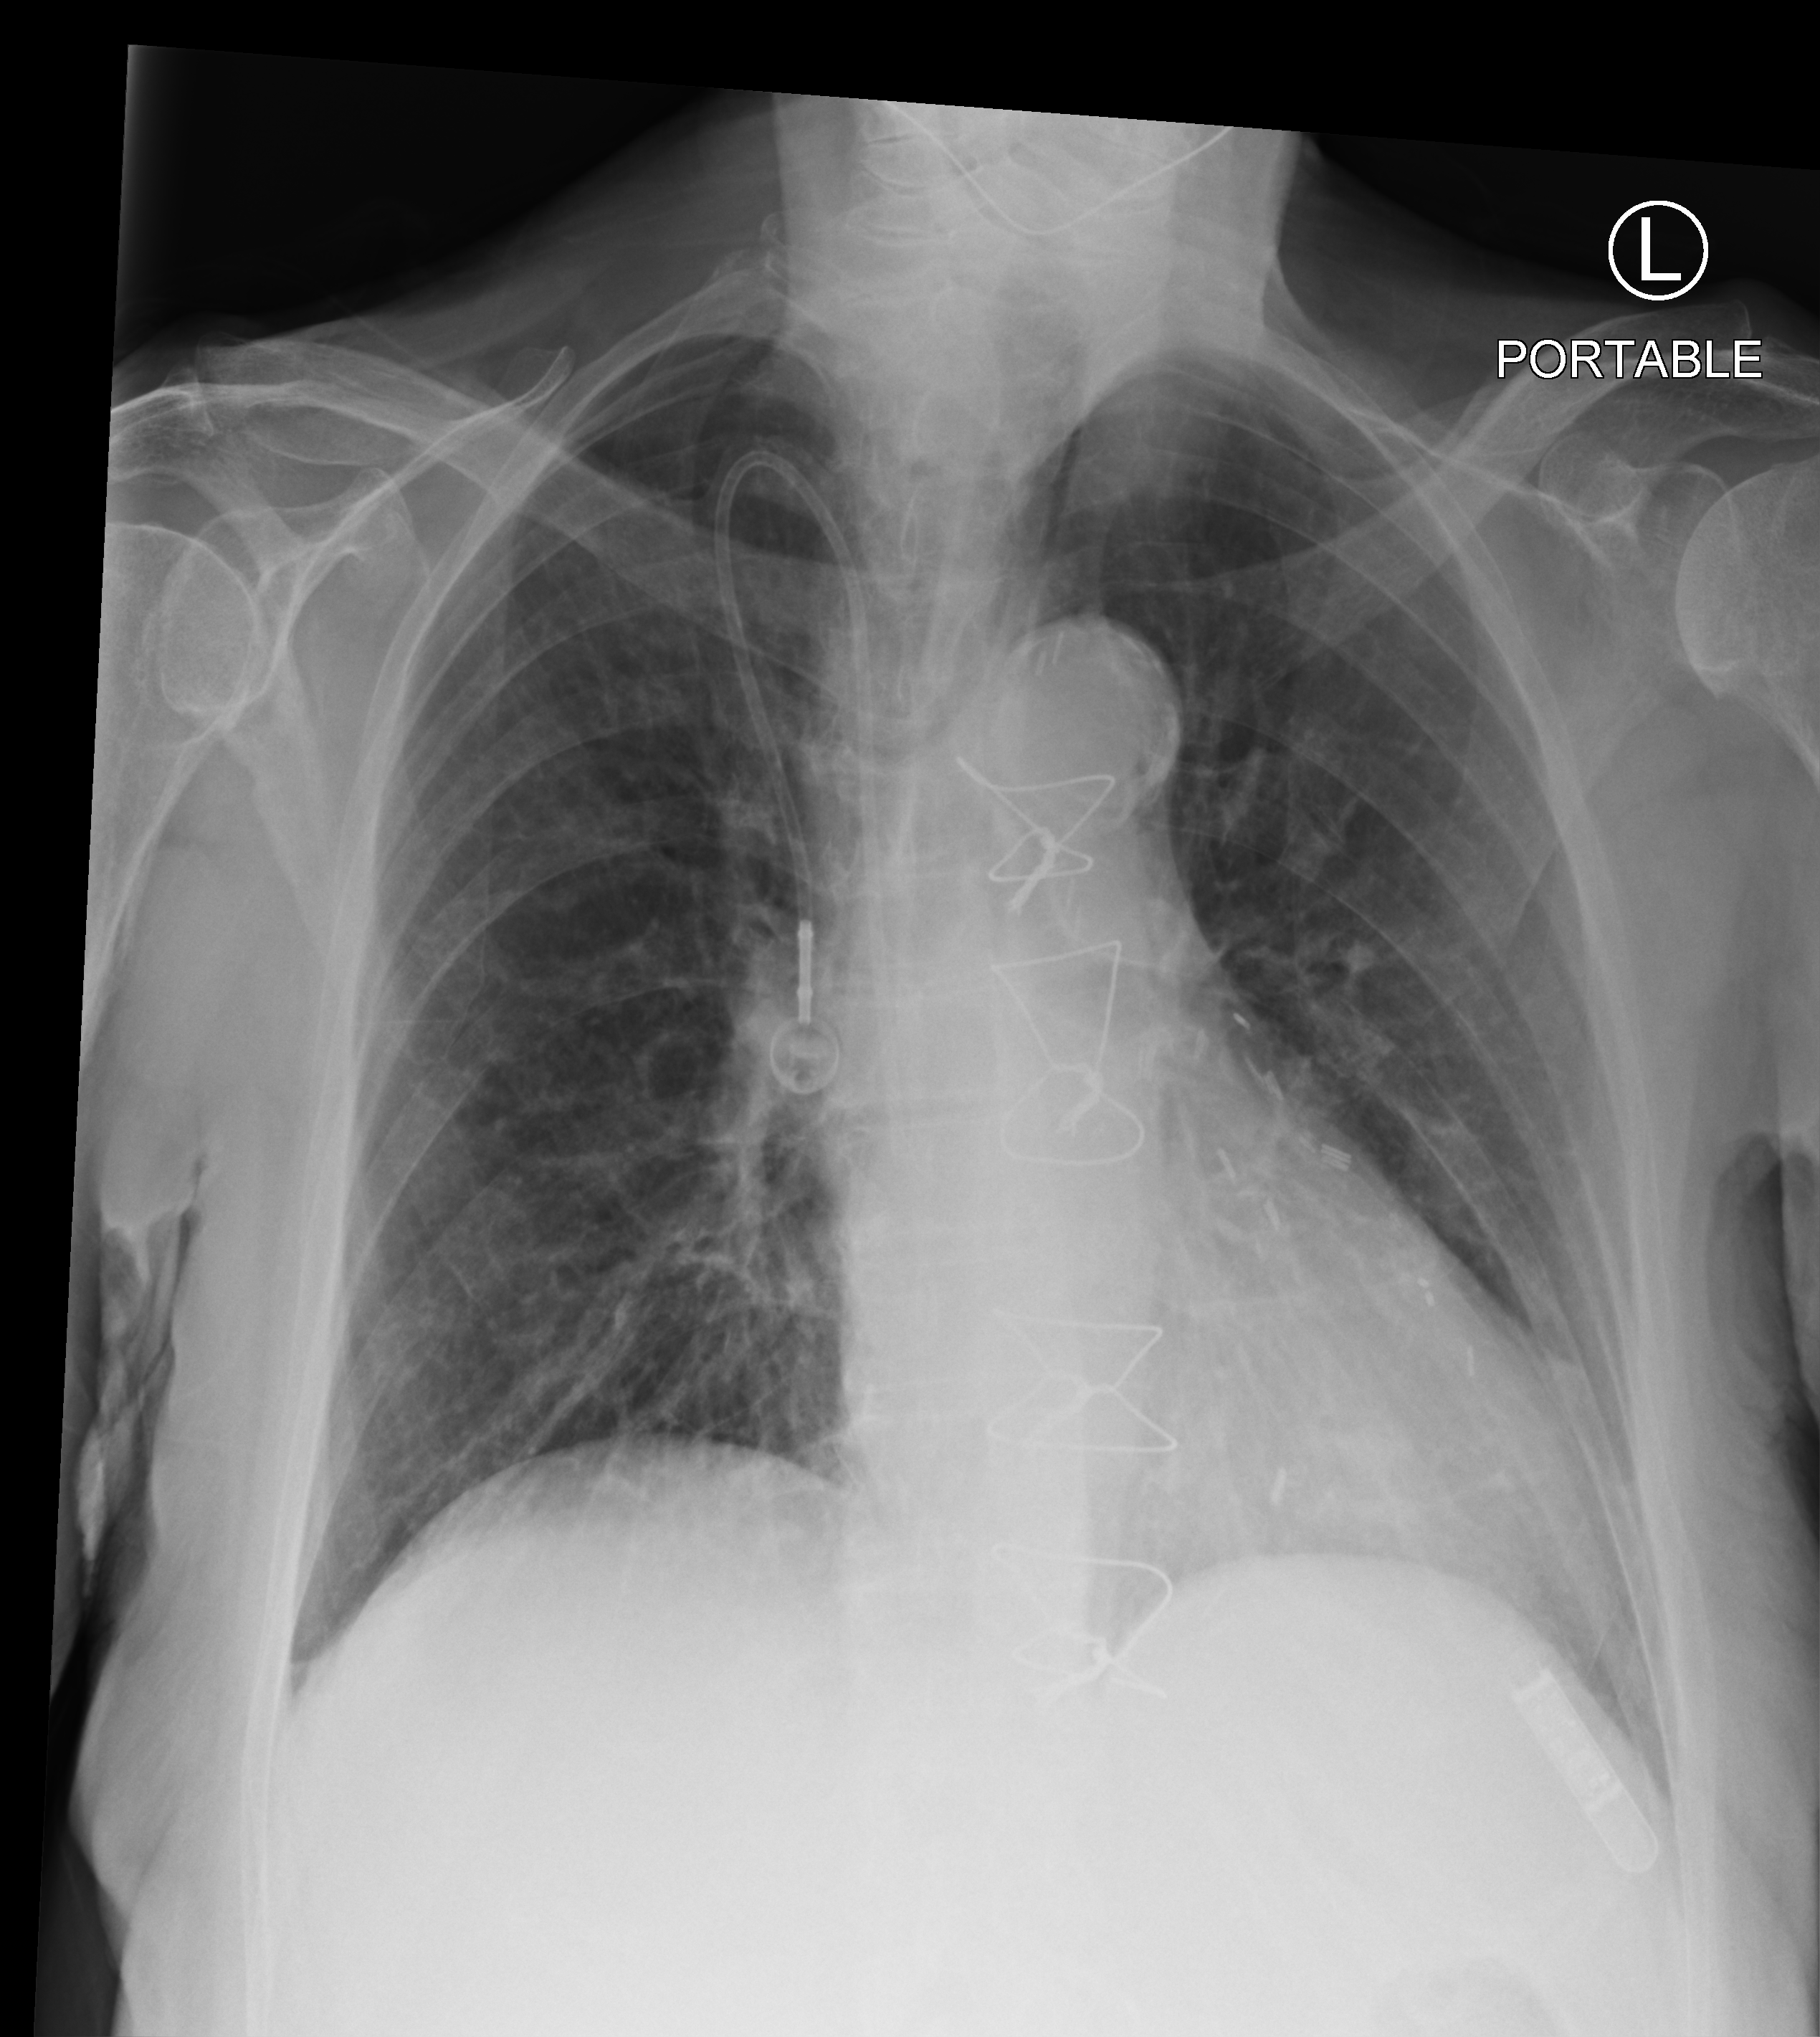
Portable chest radiograph, anteroposterior (AP) projection. Patient hospitalised with COVID-19; female, aged 75–90 years.
Hospital-stay facts (about this admission, not read from this image; timing relative to this image not recorded): mechanically ventilated during this hospital stay: no.